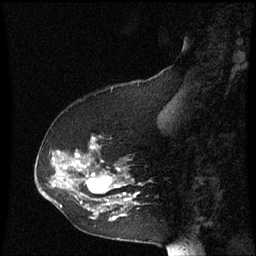
Breast MRI (dynamic contrast-enhanced), one sagittal slice. Slice 22 of 60 in the series (ordered by position). Dynamic contrast-enhanced series, image 2 of 3 at this slice position (ordered by acquisition). 1.5 T. TE 4.2 ms, TR 8.9 ms. 256 × 256 image matrix, field of view 200 × 200 mm. Female patient, age 53 years. From the clinical record (not read from this slice): setting: breast cancer imaged before/during neoadjuvant chemotherapy; receptor status: HR-positive, HER2-negative.
Annotated regions visible in this slice (semi-automatic segmentation, software-assisted and operator-edited):
- analysis volume of interest (the breast-tissue region the enhancement analysis was run in; not a lesion): box from (x=38, y=136) to (x=141, y=223) px
- tumour enhancement mask (voxels above the 70 % enhancement threshold inside the analysis volume of interest): (x=52, y=138)–(x=139, y=221)